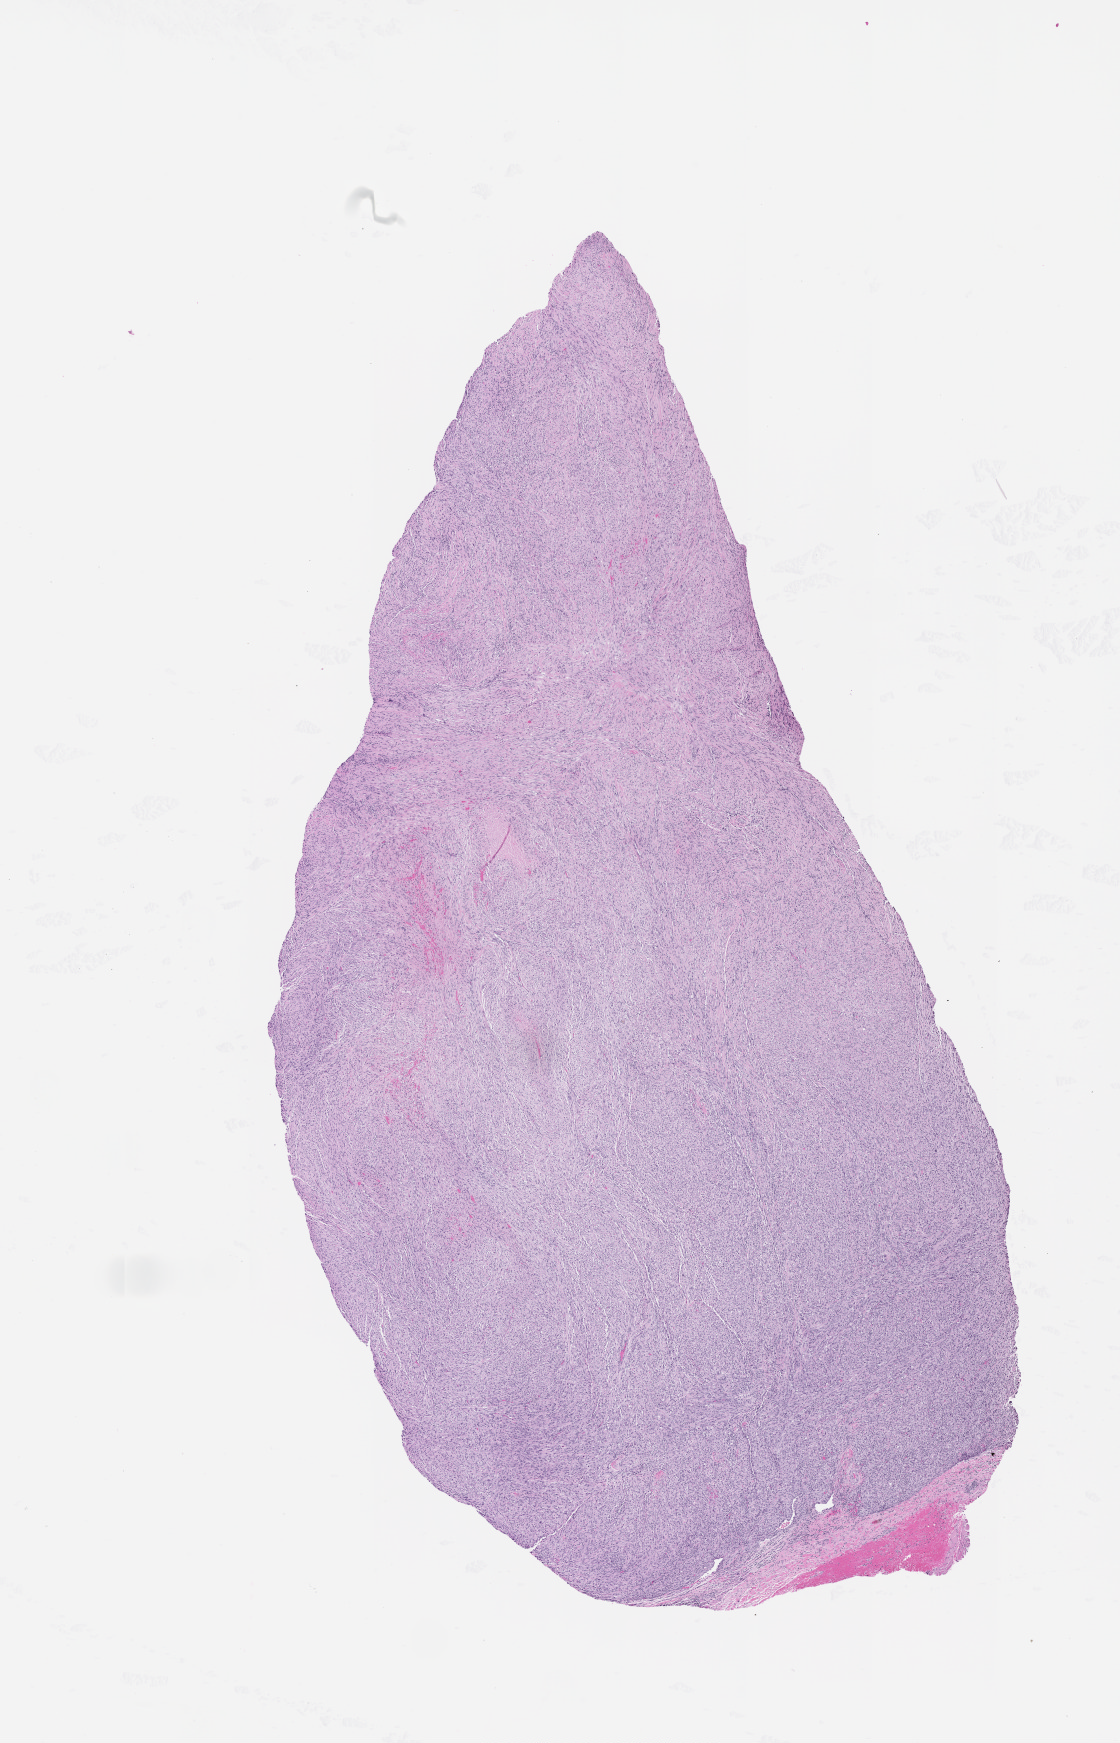
H&E-stained whole-slide image, a low-resolution overview of the entire scanned area, about 9.0 x 14.0 mm (acquisition: 20x scan).
Patient diagnosis (cohort enrolment): sarcoma (site not recorded at cohort level).